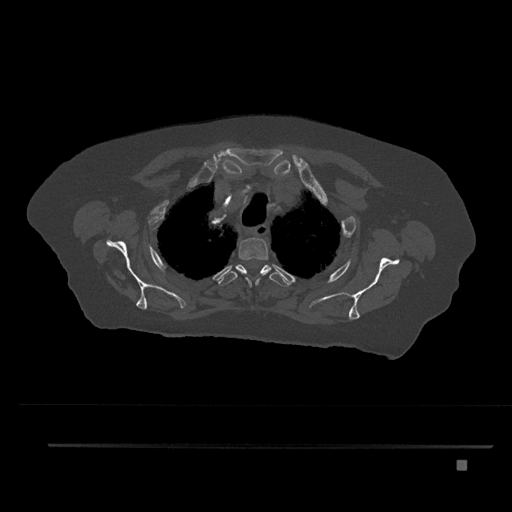
CT including the spine, one axial slice. Bone window (W 1800 / L 400 HU). 0.5 mm slice thickness. 512 × 512 image matrix. Female patient, age 76 years. Case-level facts recorded for this patient, not image findings: primary cancer: lung; vertebrae with lytic lesions (as recorded): T11, L3.
Outlined on this slice (semi-automatically segmented with operator editing):
- T2 vertebra: bounding box <236,237,271,287> (left, top, right, bottom; pixels)
- T3 vertebra: <218,264,289,287>